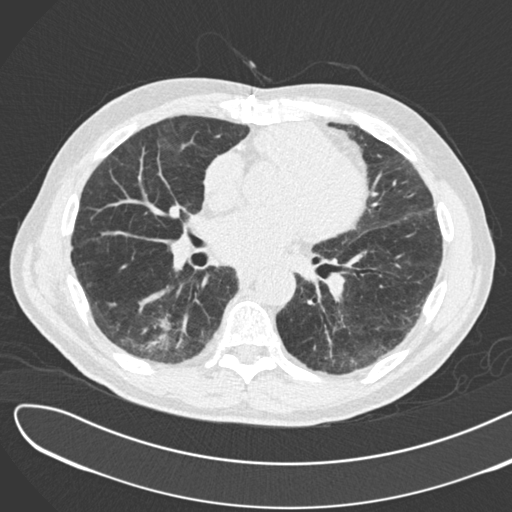
Axial slice from a low-dose chest CT screening exam. Second screening round (one year after baseline). Lung window (W 1500 / L -600 HU). 2 mm slice thickness. 512 × 512 image matrix, field of view 370 × 370 mm. Male participant, aged 72 years at enrolment. Former smoker at enrolment.
Expert reader's lesion annotation, bounding box <124,288,197,356> (left, top, right, bottom; pixels). The screening reader recorded 2 non-calcified nodules or masses ≥4 mm on this exam (right lower lobe, right lower lobe); which of them this box marks is not recorded. Participant outcome: lung cancer diagnosed 46 days after this screen — squamous cell carcinoma, NOS, right lower lobe, poorly differentiated (G3), stage IB (AJCC 6th edition), 42 mm at pathology.